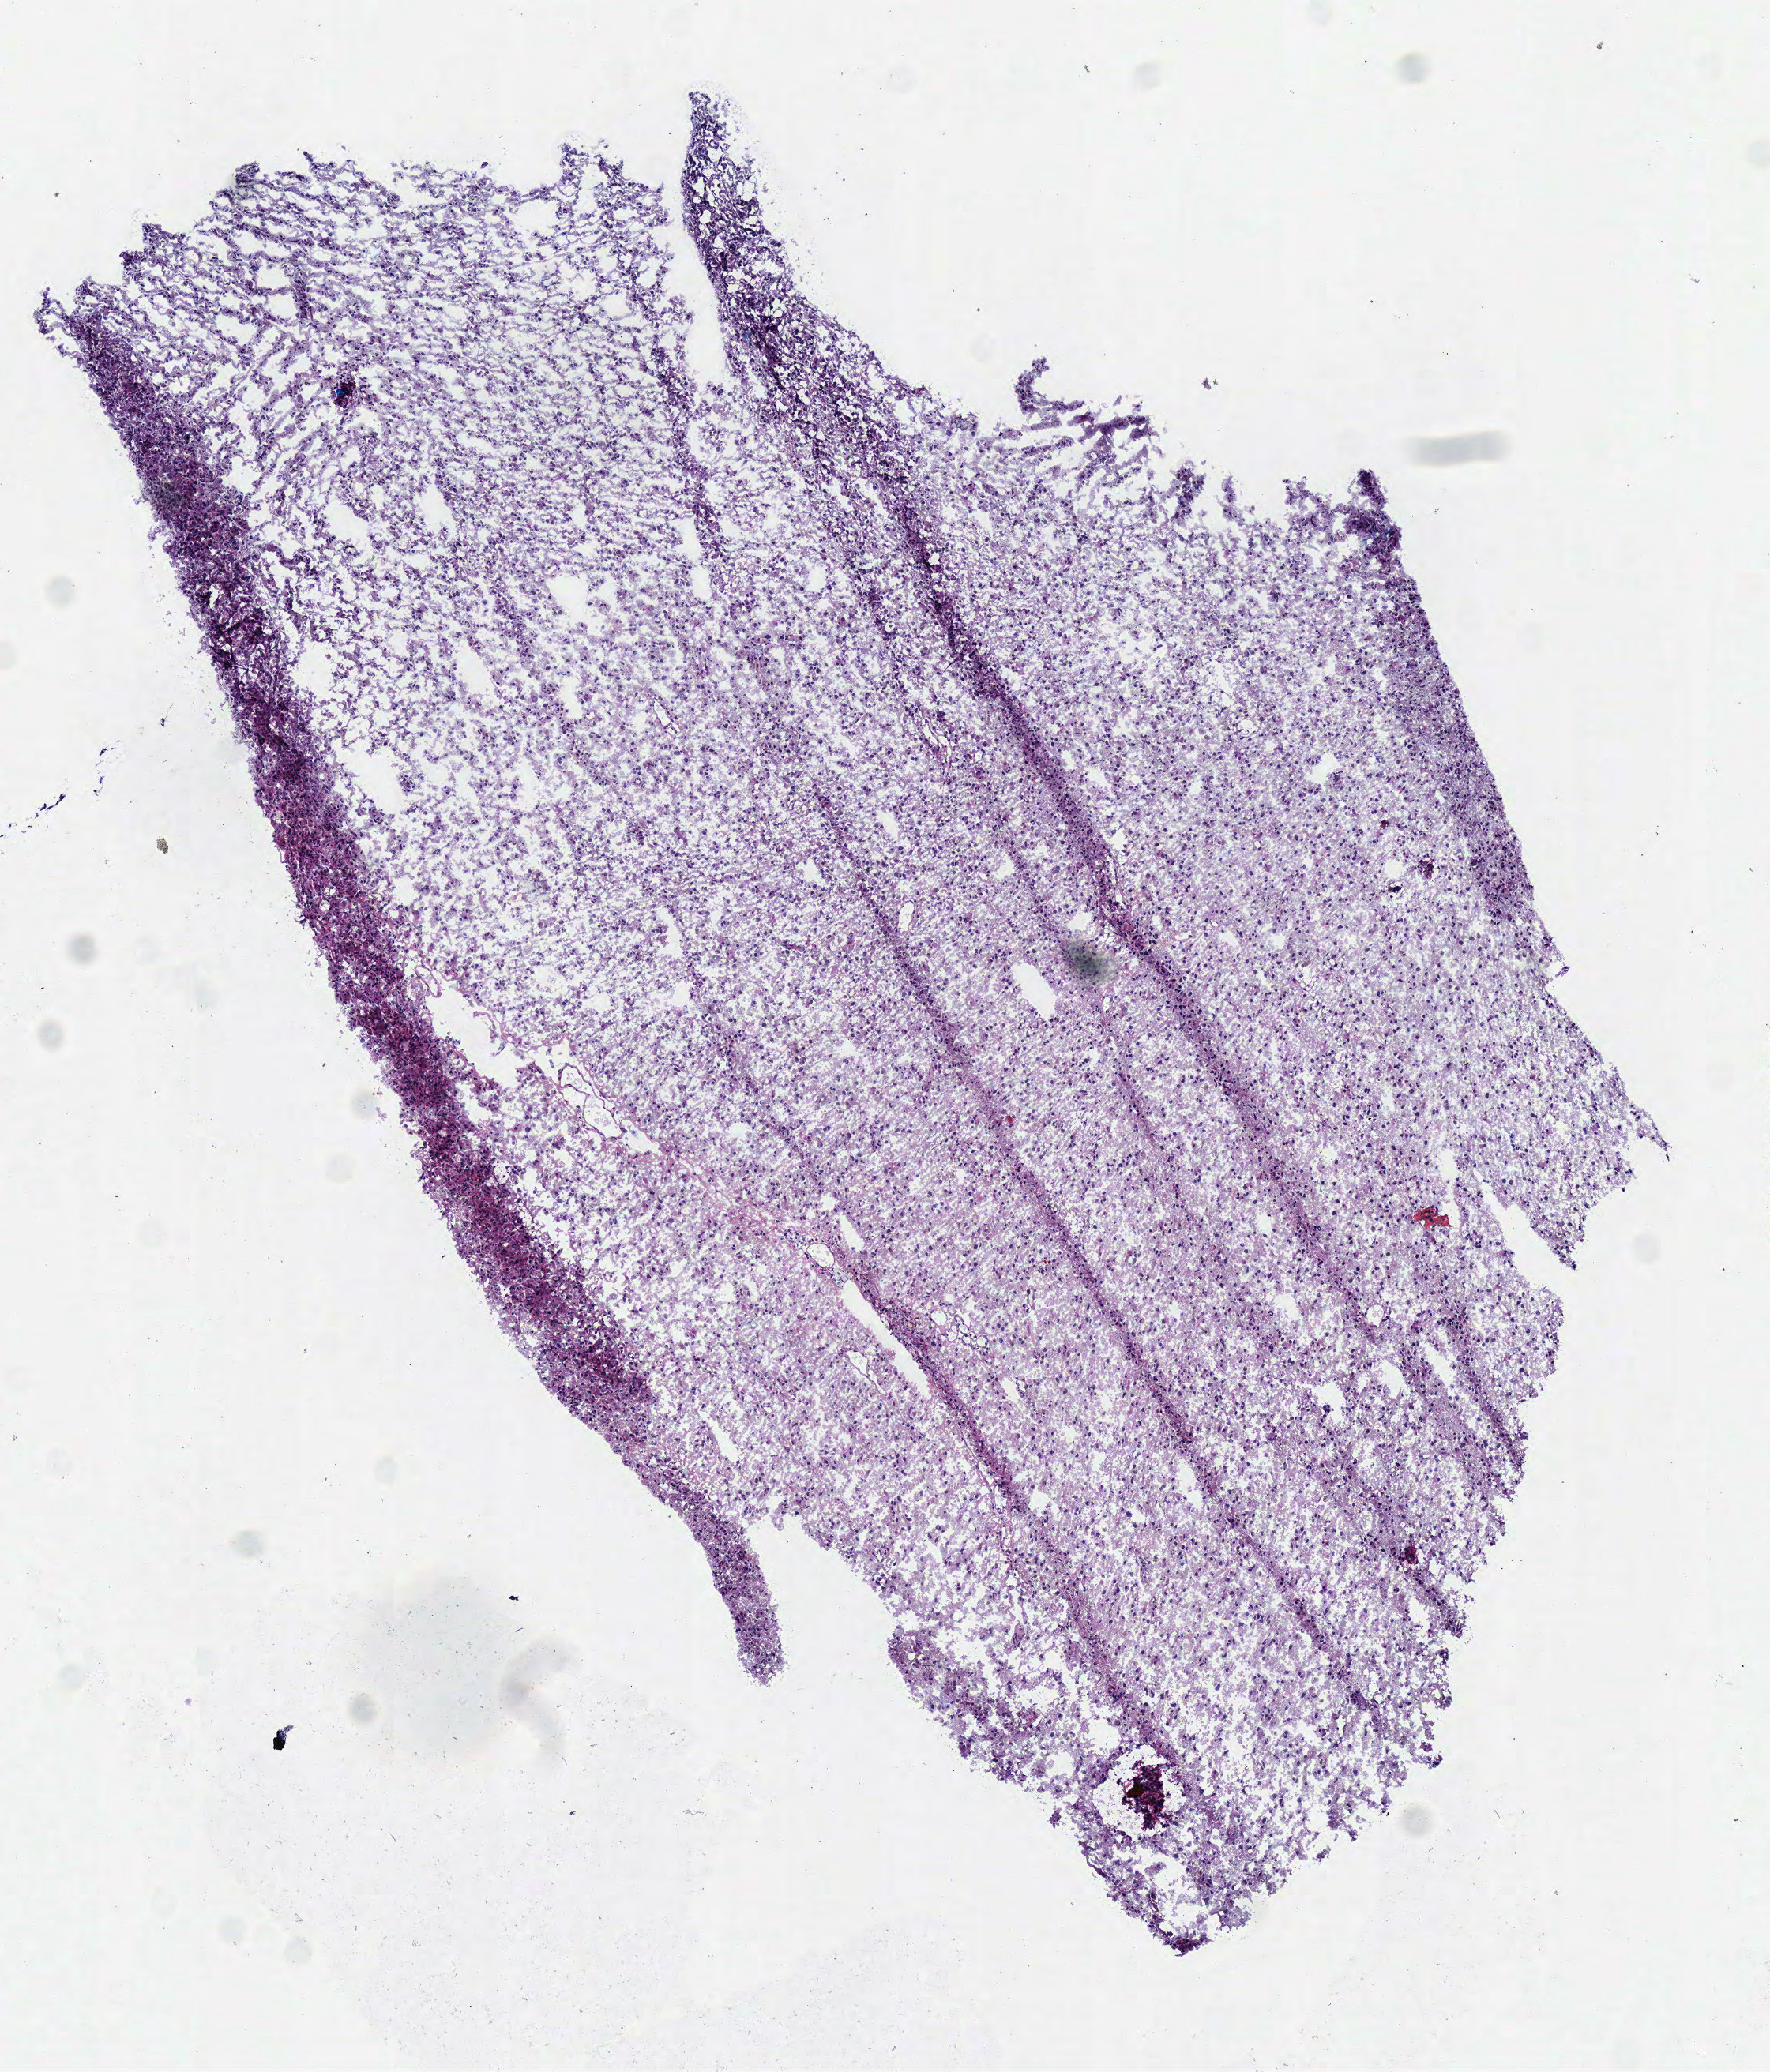
Hematoxylin and eosin (H&E) stained whole-slide image — whole scanned area (about 4.4 x 5.2 mm, from a 40x scan) shown as a low-resolution overview, frozen section from the bottom of the tissue portion, primary tumour sample from the brain. Male, age 70 years at initial diagnosis. Histologic grade: G2 (moderately differentiated). Composition of this section per pathologist review: tumour cells 100%, tumour nuclei 75%, normal cells 0%, stromal cells 0%, necrosis 0%.
* diagnosis: Oligodendroglioma, NOS